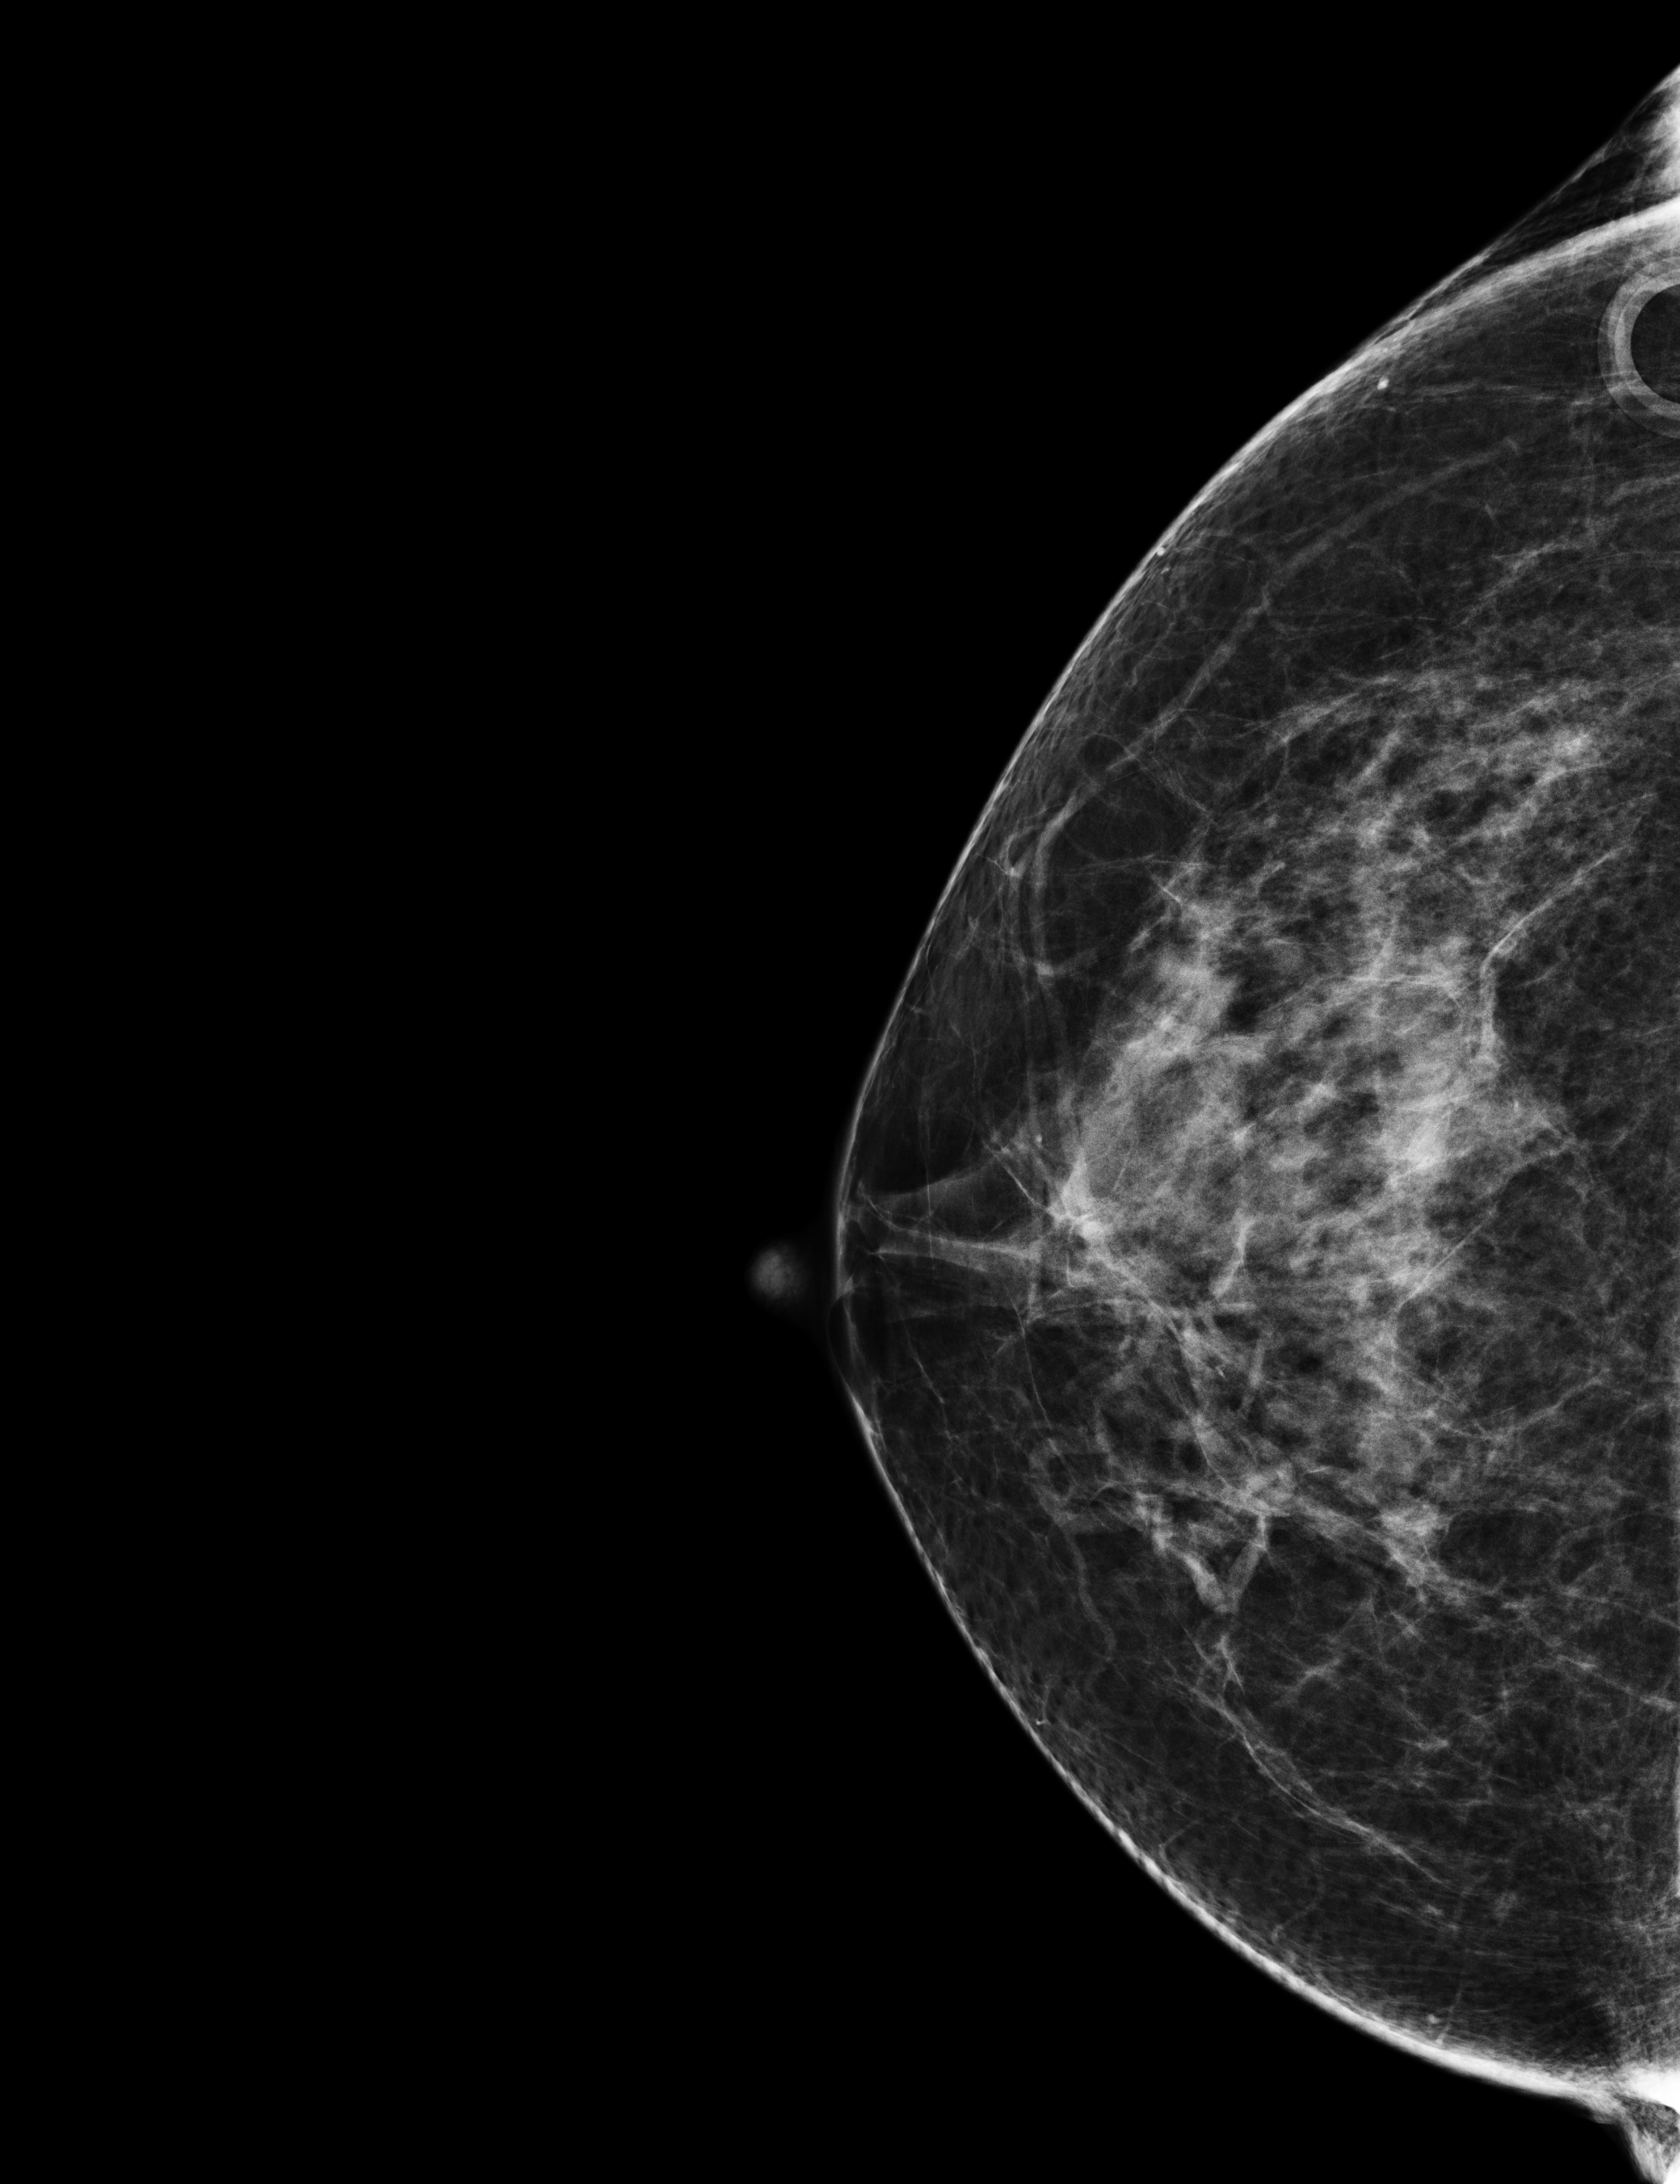
Full-field digital mammogram (FFDM), right breast, CC view, screening examination, compressed breast thickness 68 mm. Female patient, age 53 years.
- BI-RADS breast density category at the screening exam (both breasts, scale 1–4): 3
- final BI-RADS assessment for this screening round (tomosynthesis exam, both breasts): category 1
- recall: no recall after this screen